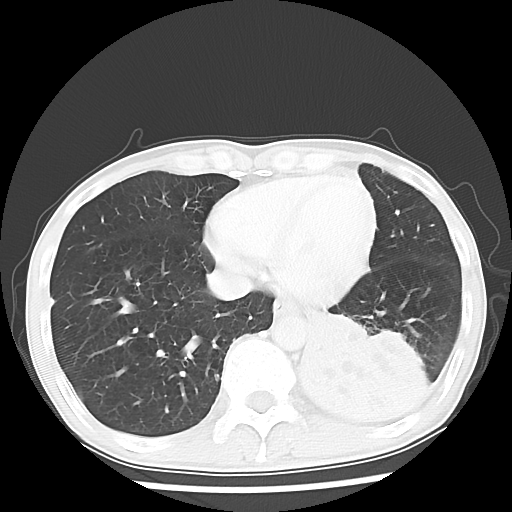
Chest CT, one axial slice. Position 17 of 64 along the scan axis. 120 kVp. Lung window (W 1500 / L -600 HU). 5 mm slice thickness. 512 × 512 image matrix. Male patient, age 68 years. From the clinical record (not read from this slice): clinical TNM (as recorded): T4 N0 M0.
Outlined on this slice (rectangle marked by the reading radiologist):
- lung tumour (recorded histology: squamous cell carcinoma): box from (x=287, y=308) to (x=425, y=424) px